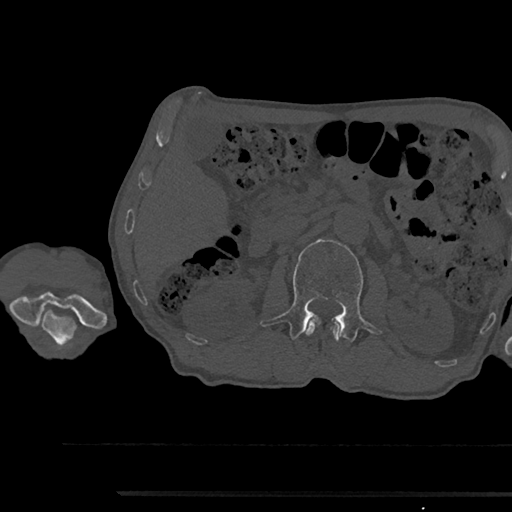
CT including the spine, one axial slice. Slice 584 of 797 in the series (ordered by position). Reconstruction kernel Br40s/3. 120 kVp. Bone window (W 1800 / L 400 HU). 512 × 512 image matrix, field of view 367 × 367 mm. Male patient, age 79 years. From the clinical record (not read from this slice): primary cancer: prostate.
Structures marked on this image (semi-automatically segmented with operator editing):
- L1 vertebra: bounding box (x1, y1, x2, y2) in pixels: (305, 318, 342, 342)
- L2 vertebra: (260, 239, 379, 341)